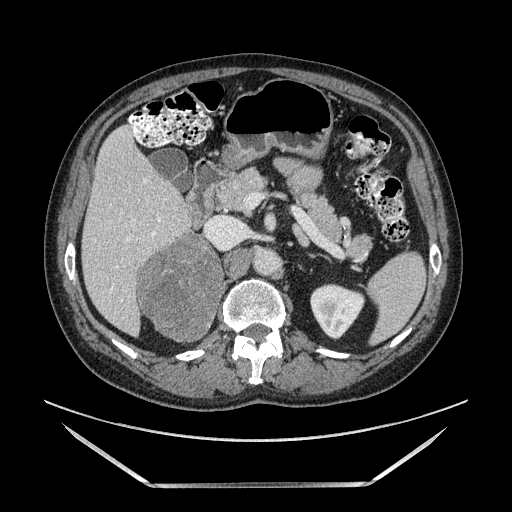
Contrast-enhanced abdominal CT, one axial slice. Position 76 of 185 along the scan axis. Soft-tissue window (W 400 / L 40 HU). 512 × 512 image matrix, field of view 440 × 440 mm. Male patient. From the clinical record (not read from this slice): diagnosis: adrenocortical carcinoma; tumour side: right adrenal; tumour size at pathology: 10.3 cm; Ki-67 index: 20 %; stage (as recorded): 3.
Structures marked on this image (semi-automatically segmented with operator editing):
- mass: bounding box [x1, y1, x2, y2] px = [140, 236, 220, 339]